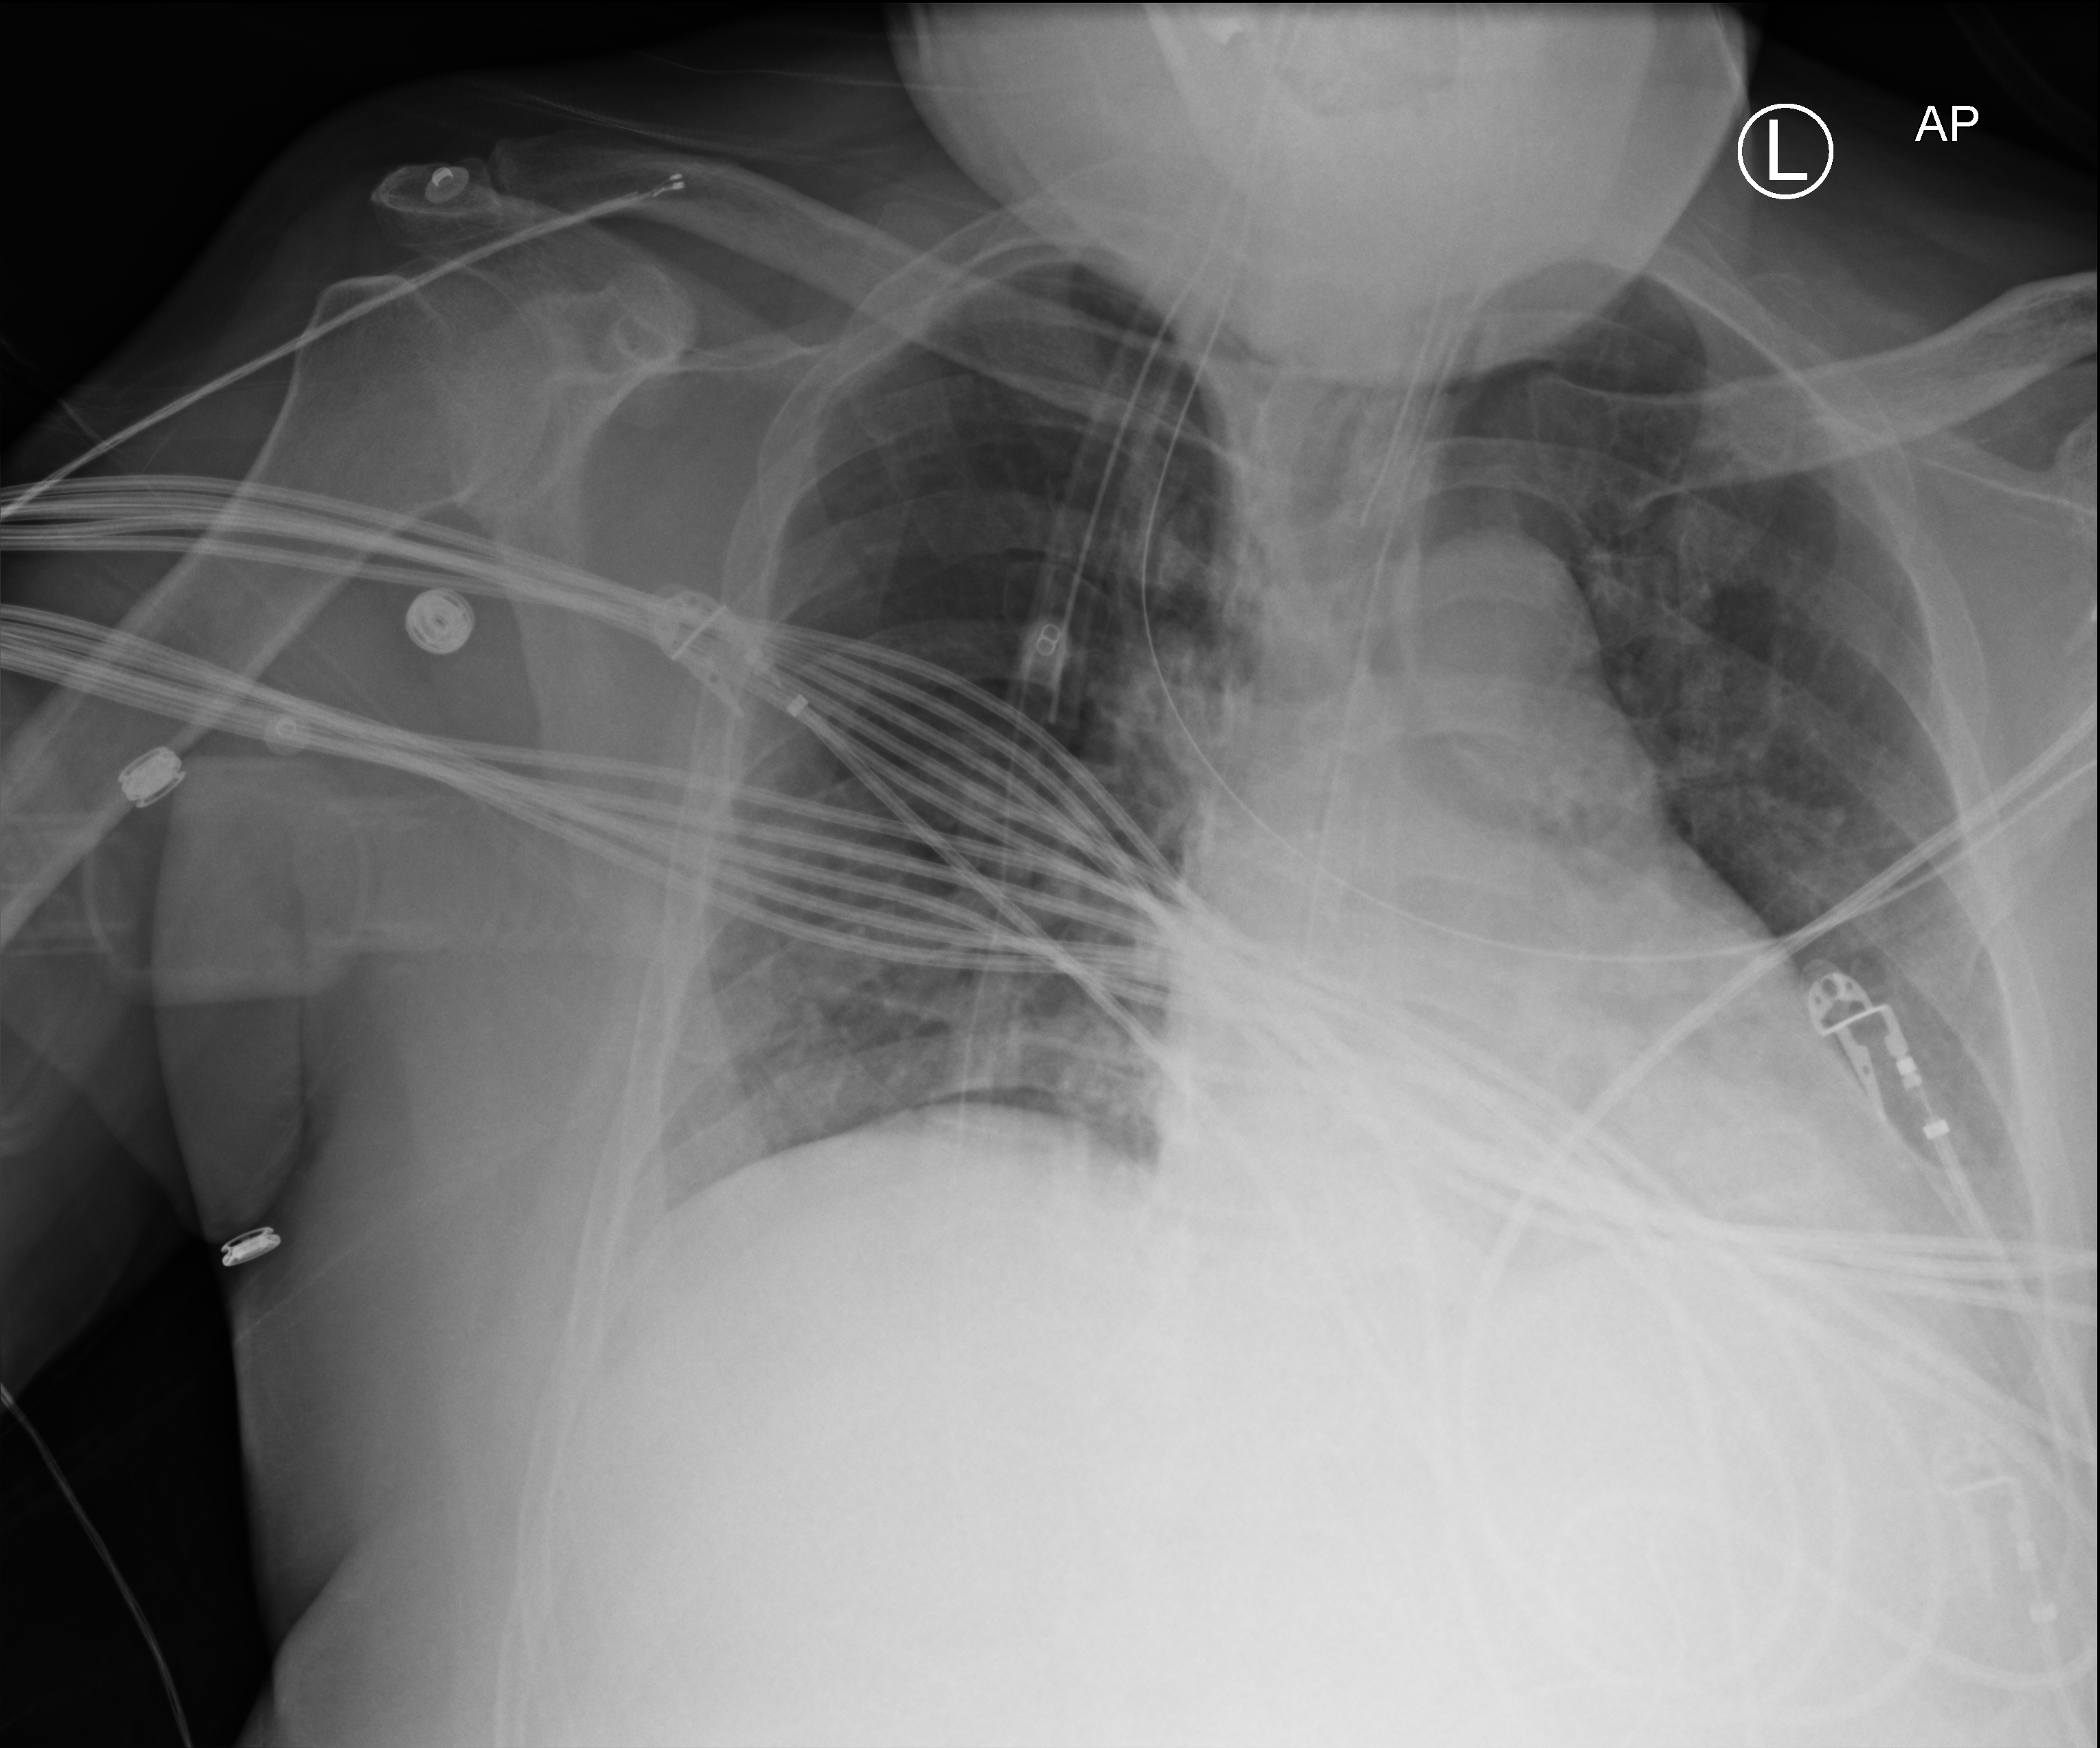
Chest X-ray (portable); anteroposterior (AP) projection. Patient hospitalised with COVID-19, aged 18–59 years.
From the hospital-stay record, not from the radiograph (when in the stay this image was taken is not recorded):
- admitted to intensive care during this hospital stay: yes
- length of hospital stay: 37 days